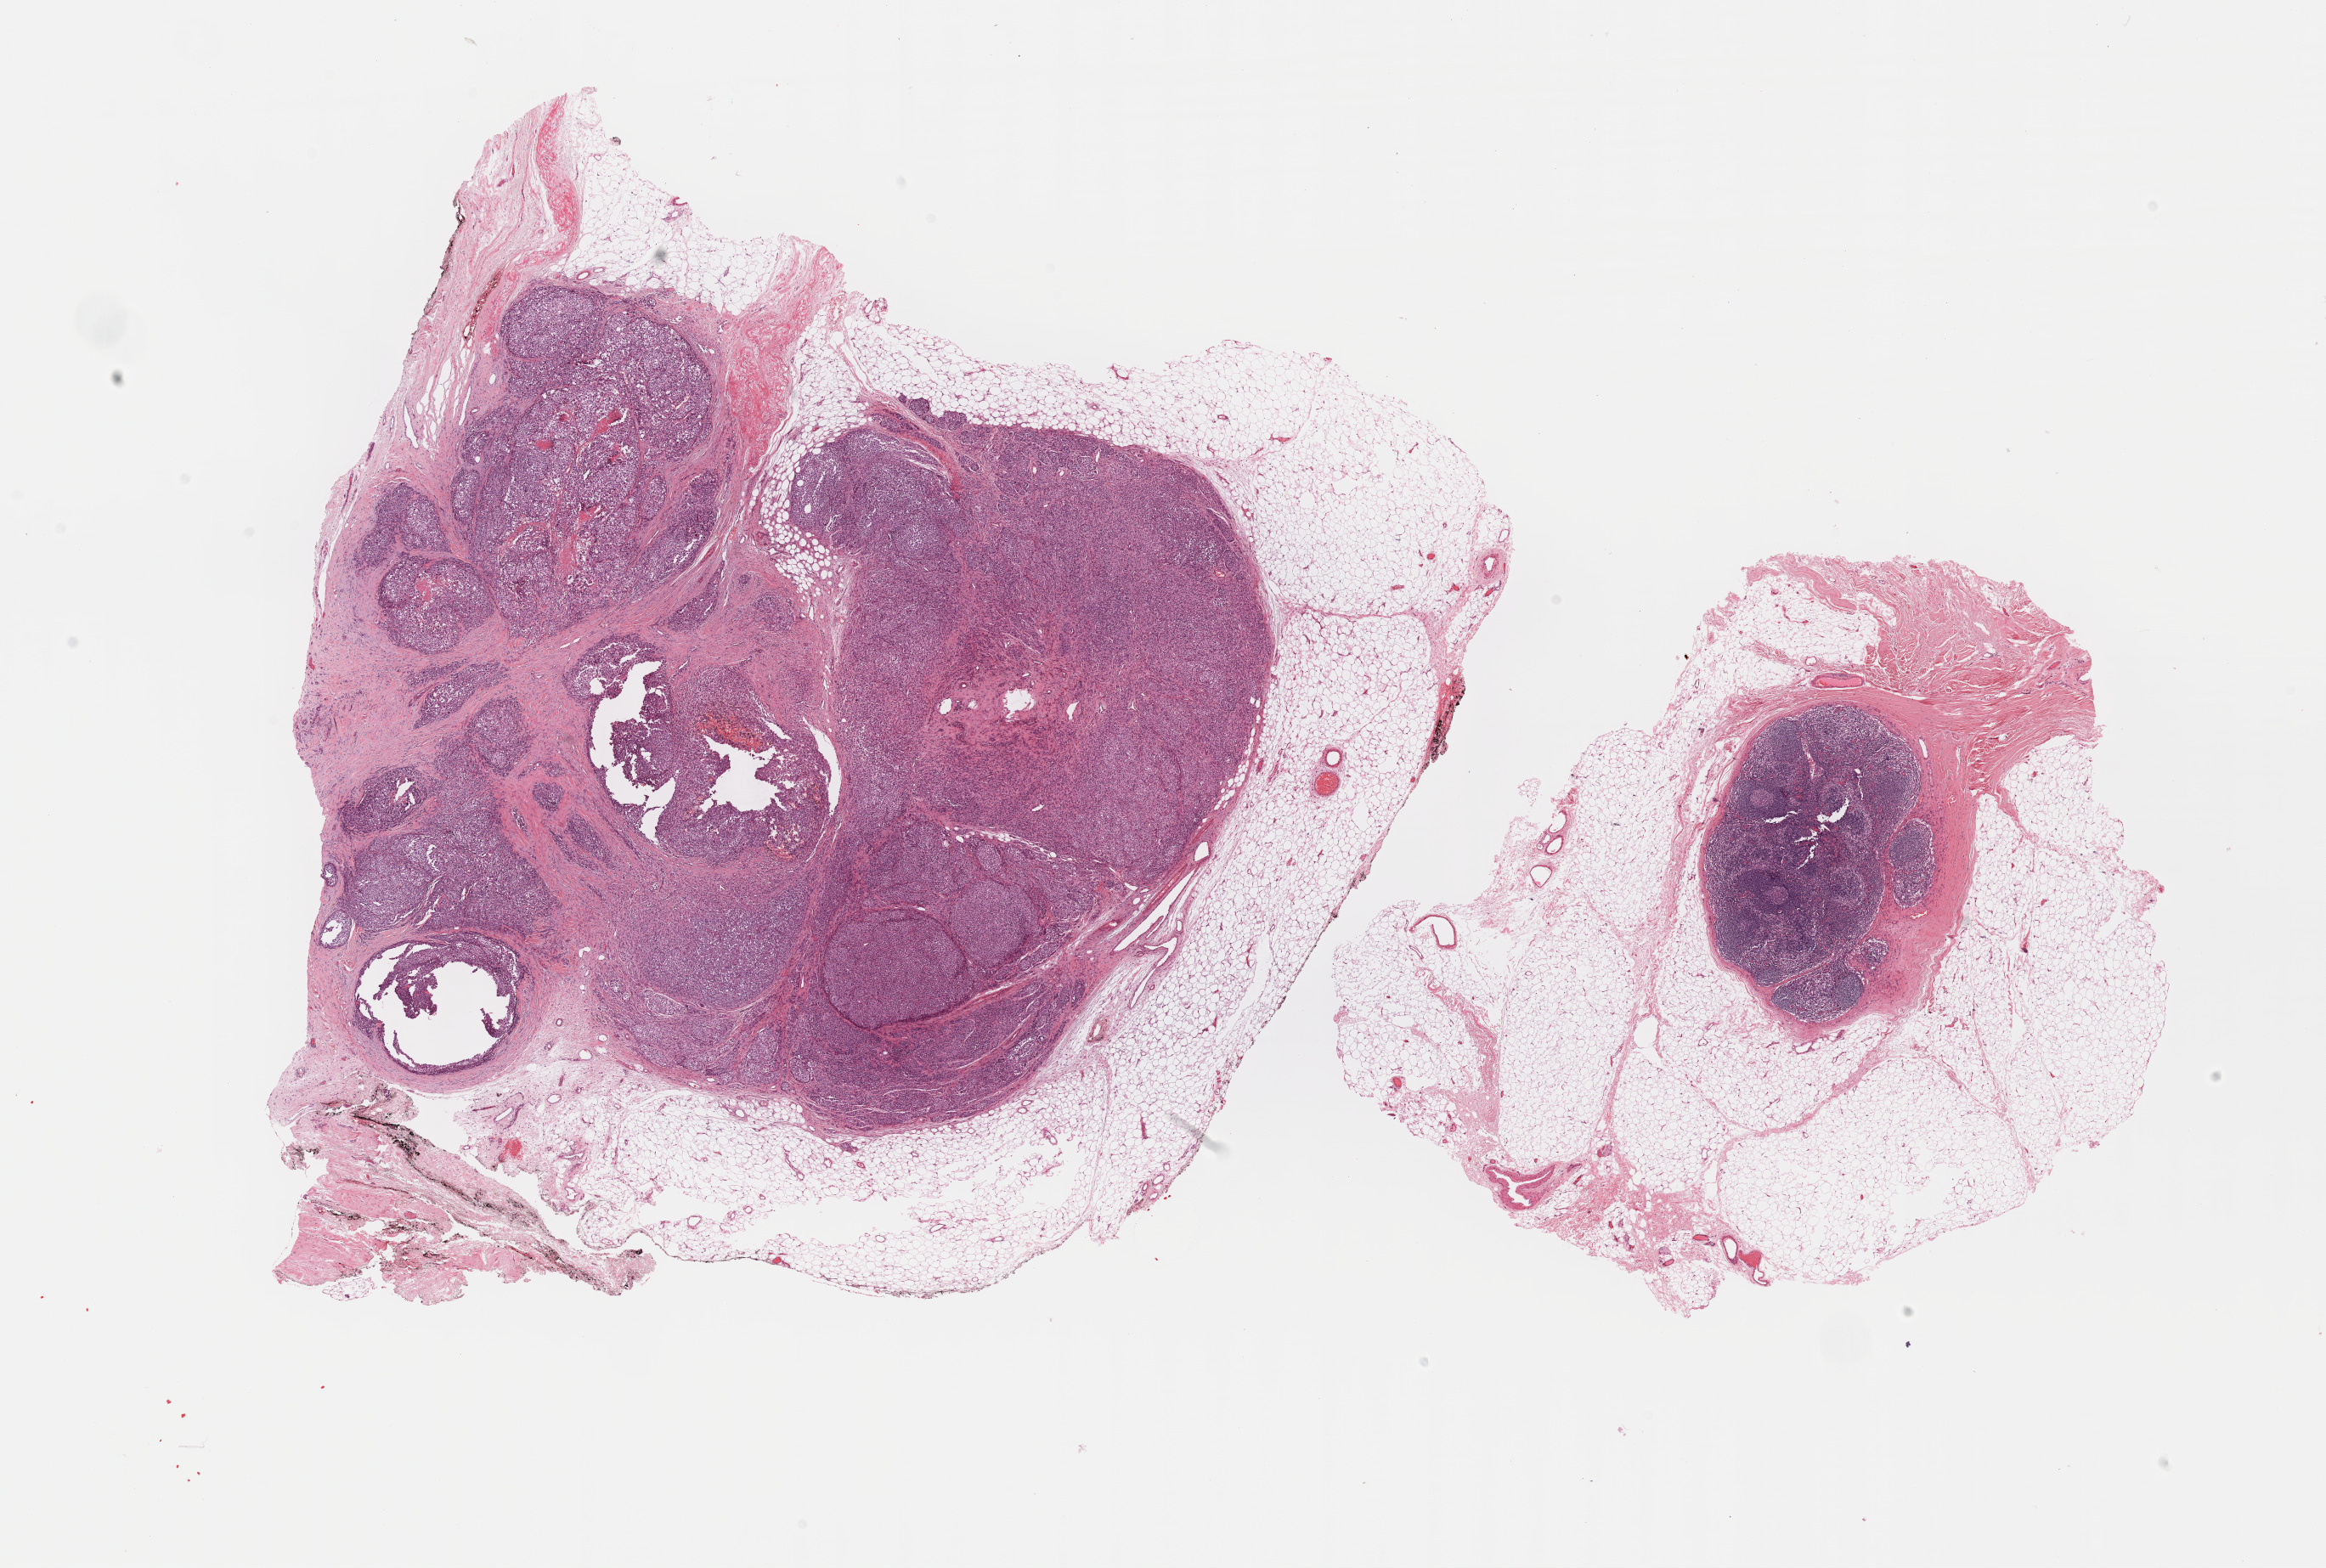
Whole-slide histology image, H&E — shown as a low-resolution overview of the whole scanned area (about 22.1 x 14.9 mm, slide scanned at 40x), formalin-fixed paraffin-embedded (FFPE) diagnostic section, metastatic tumour sample. Male patient; age at initial diagnosis 48 years.
This section: metastatic tumour tissue. Patient diagnosis: Nodular melanoma.